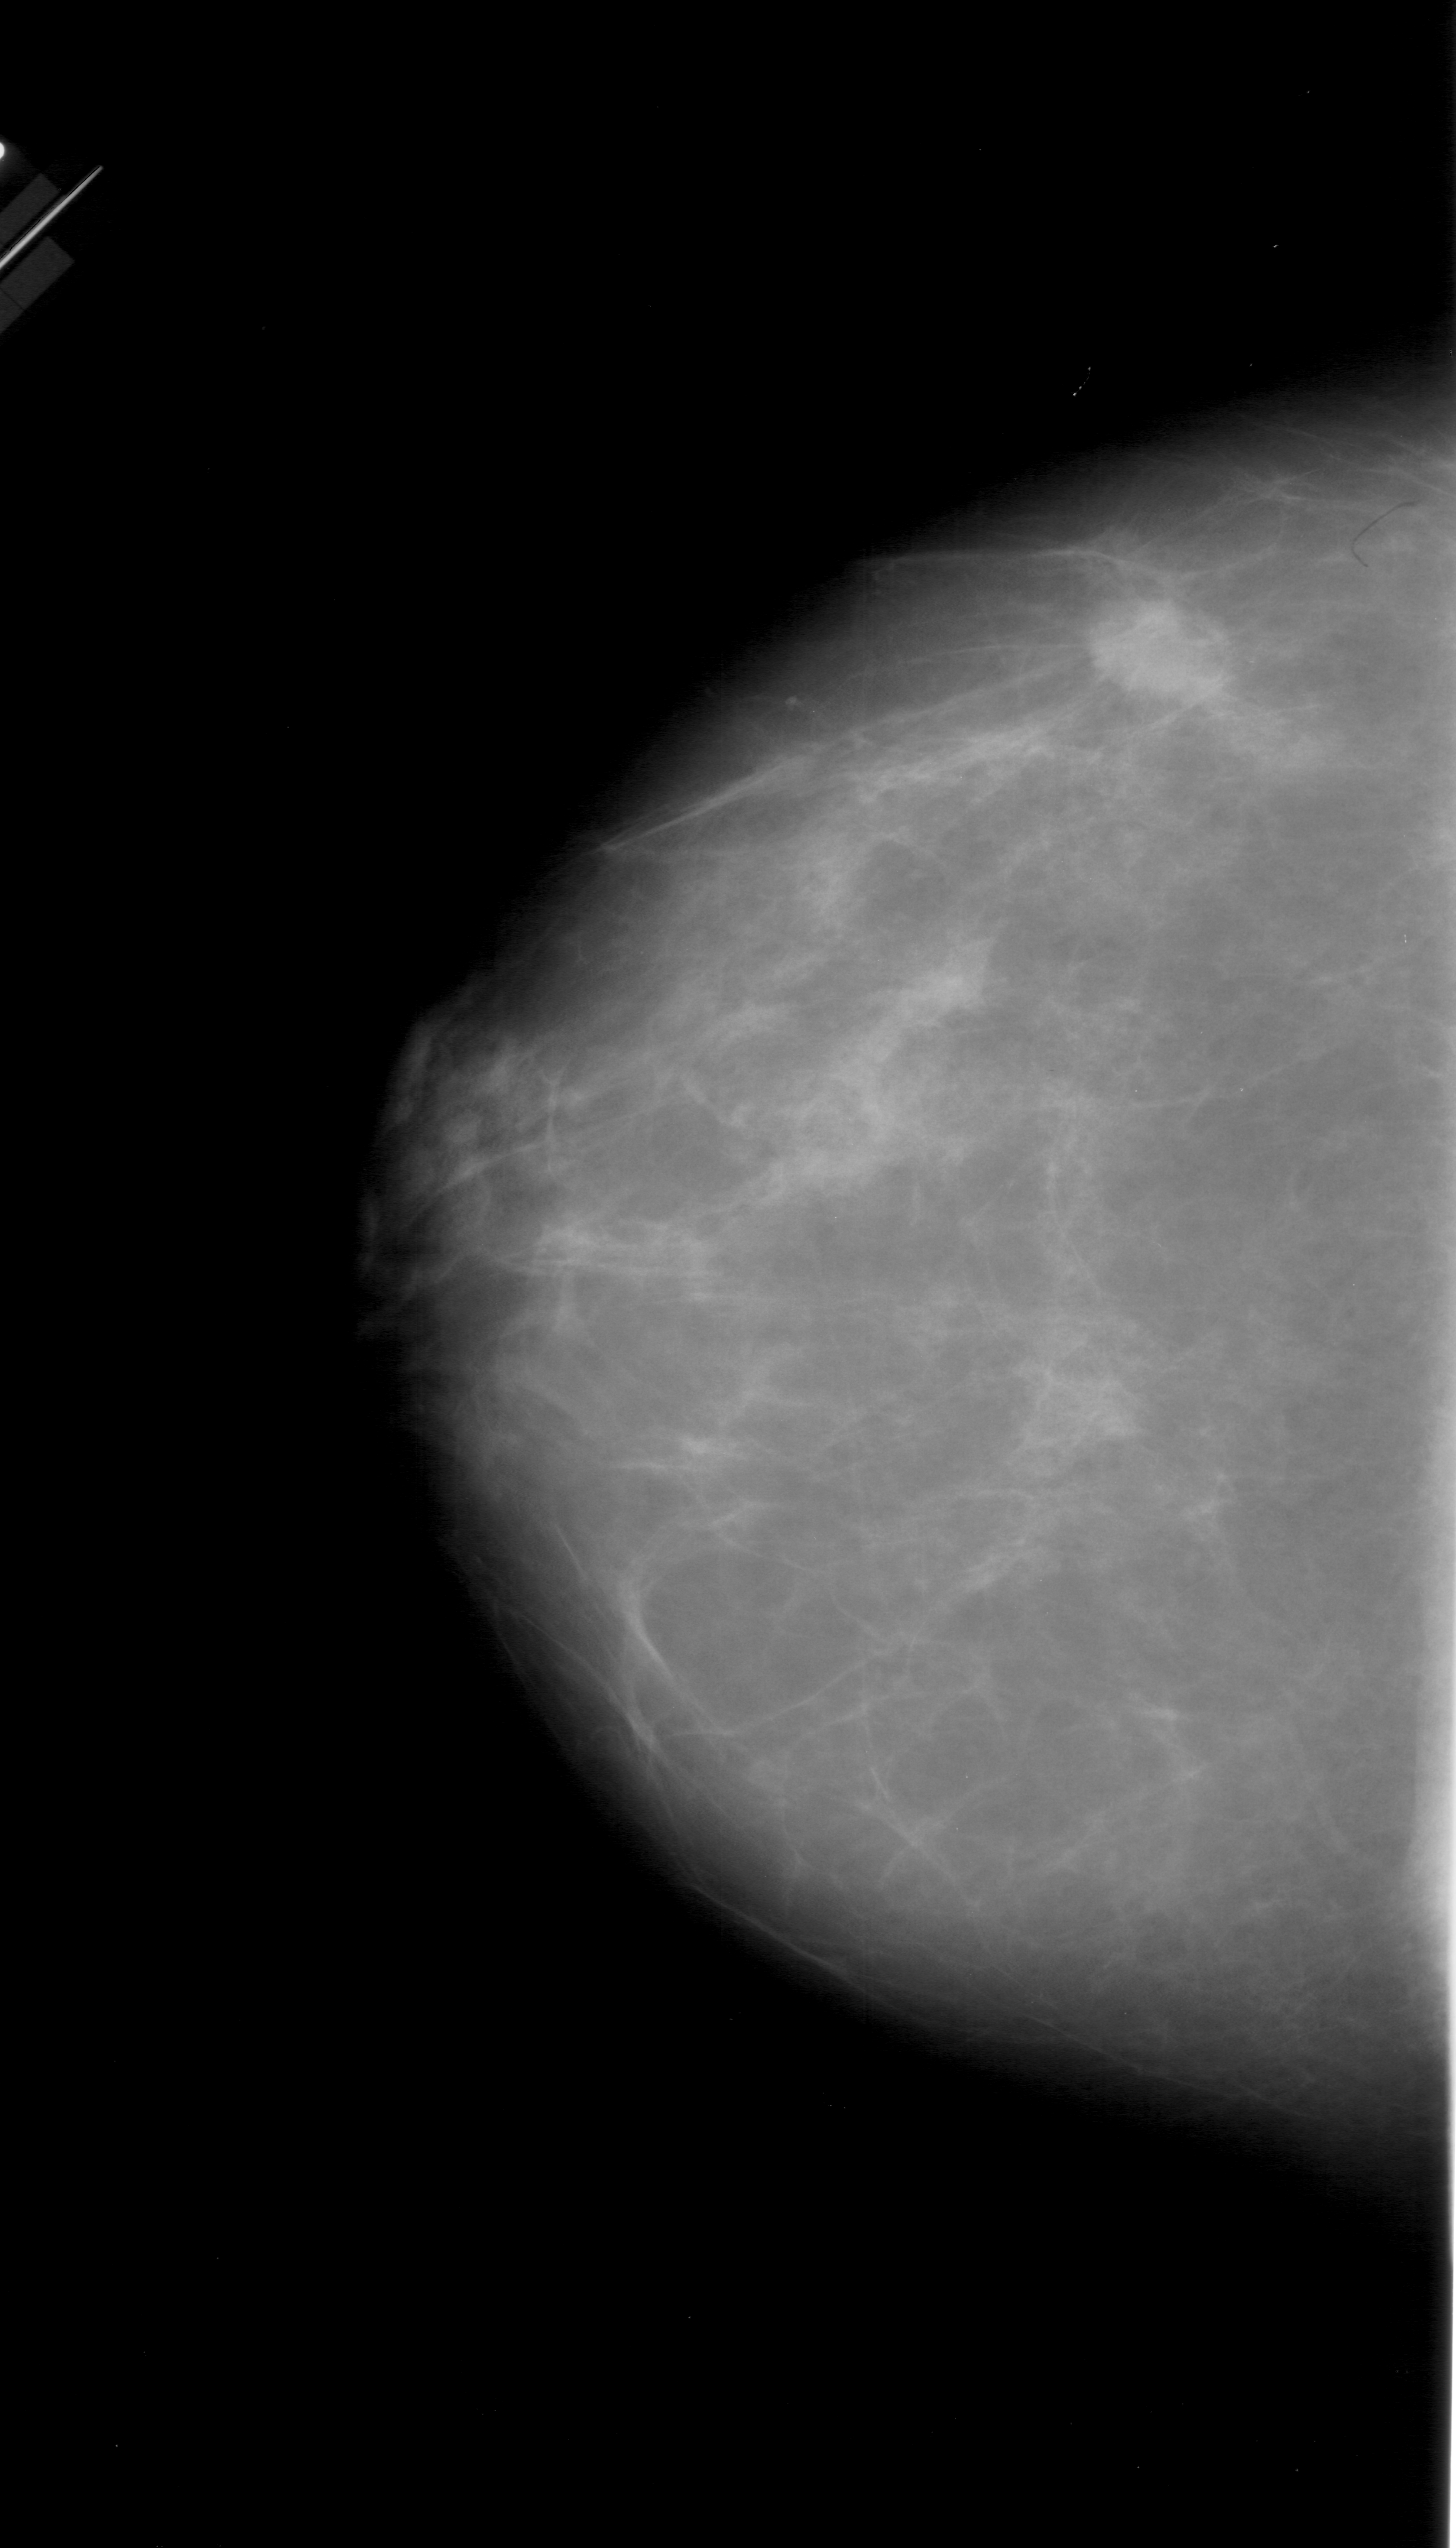
Scanned film-screen mammogram; left breast; CC view; 1456 × 2548 image matrix.
Marked abnormalities (boxes around the expert regions of interest):
- mass, shape irregular, margins spiculated; BI-RADS assessment category 5; subtlety rating 4 on a 1 (subtle) to 5 (obvious) scale; pathology result (as recorded, not read from the image): malignant: bounding box [x1, y1, x2, y2] px = [1057, 567, 1249, 708]